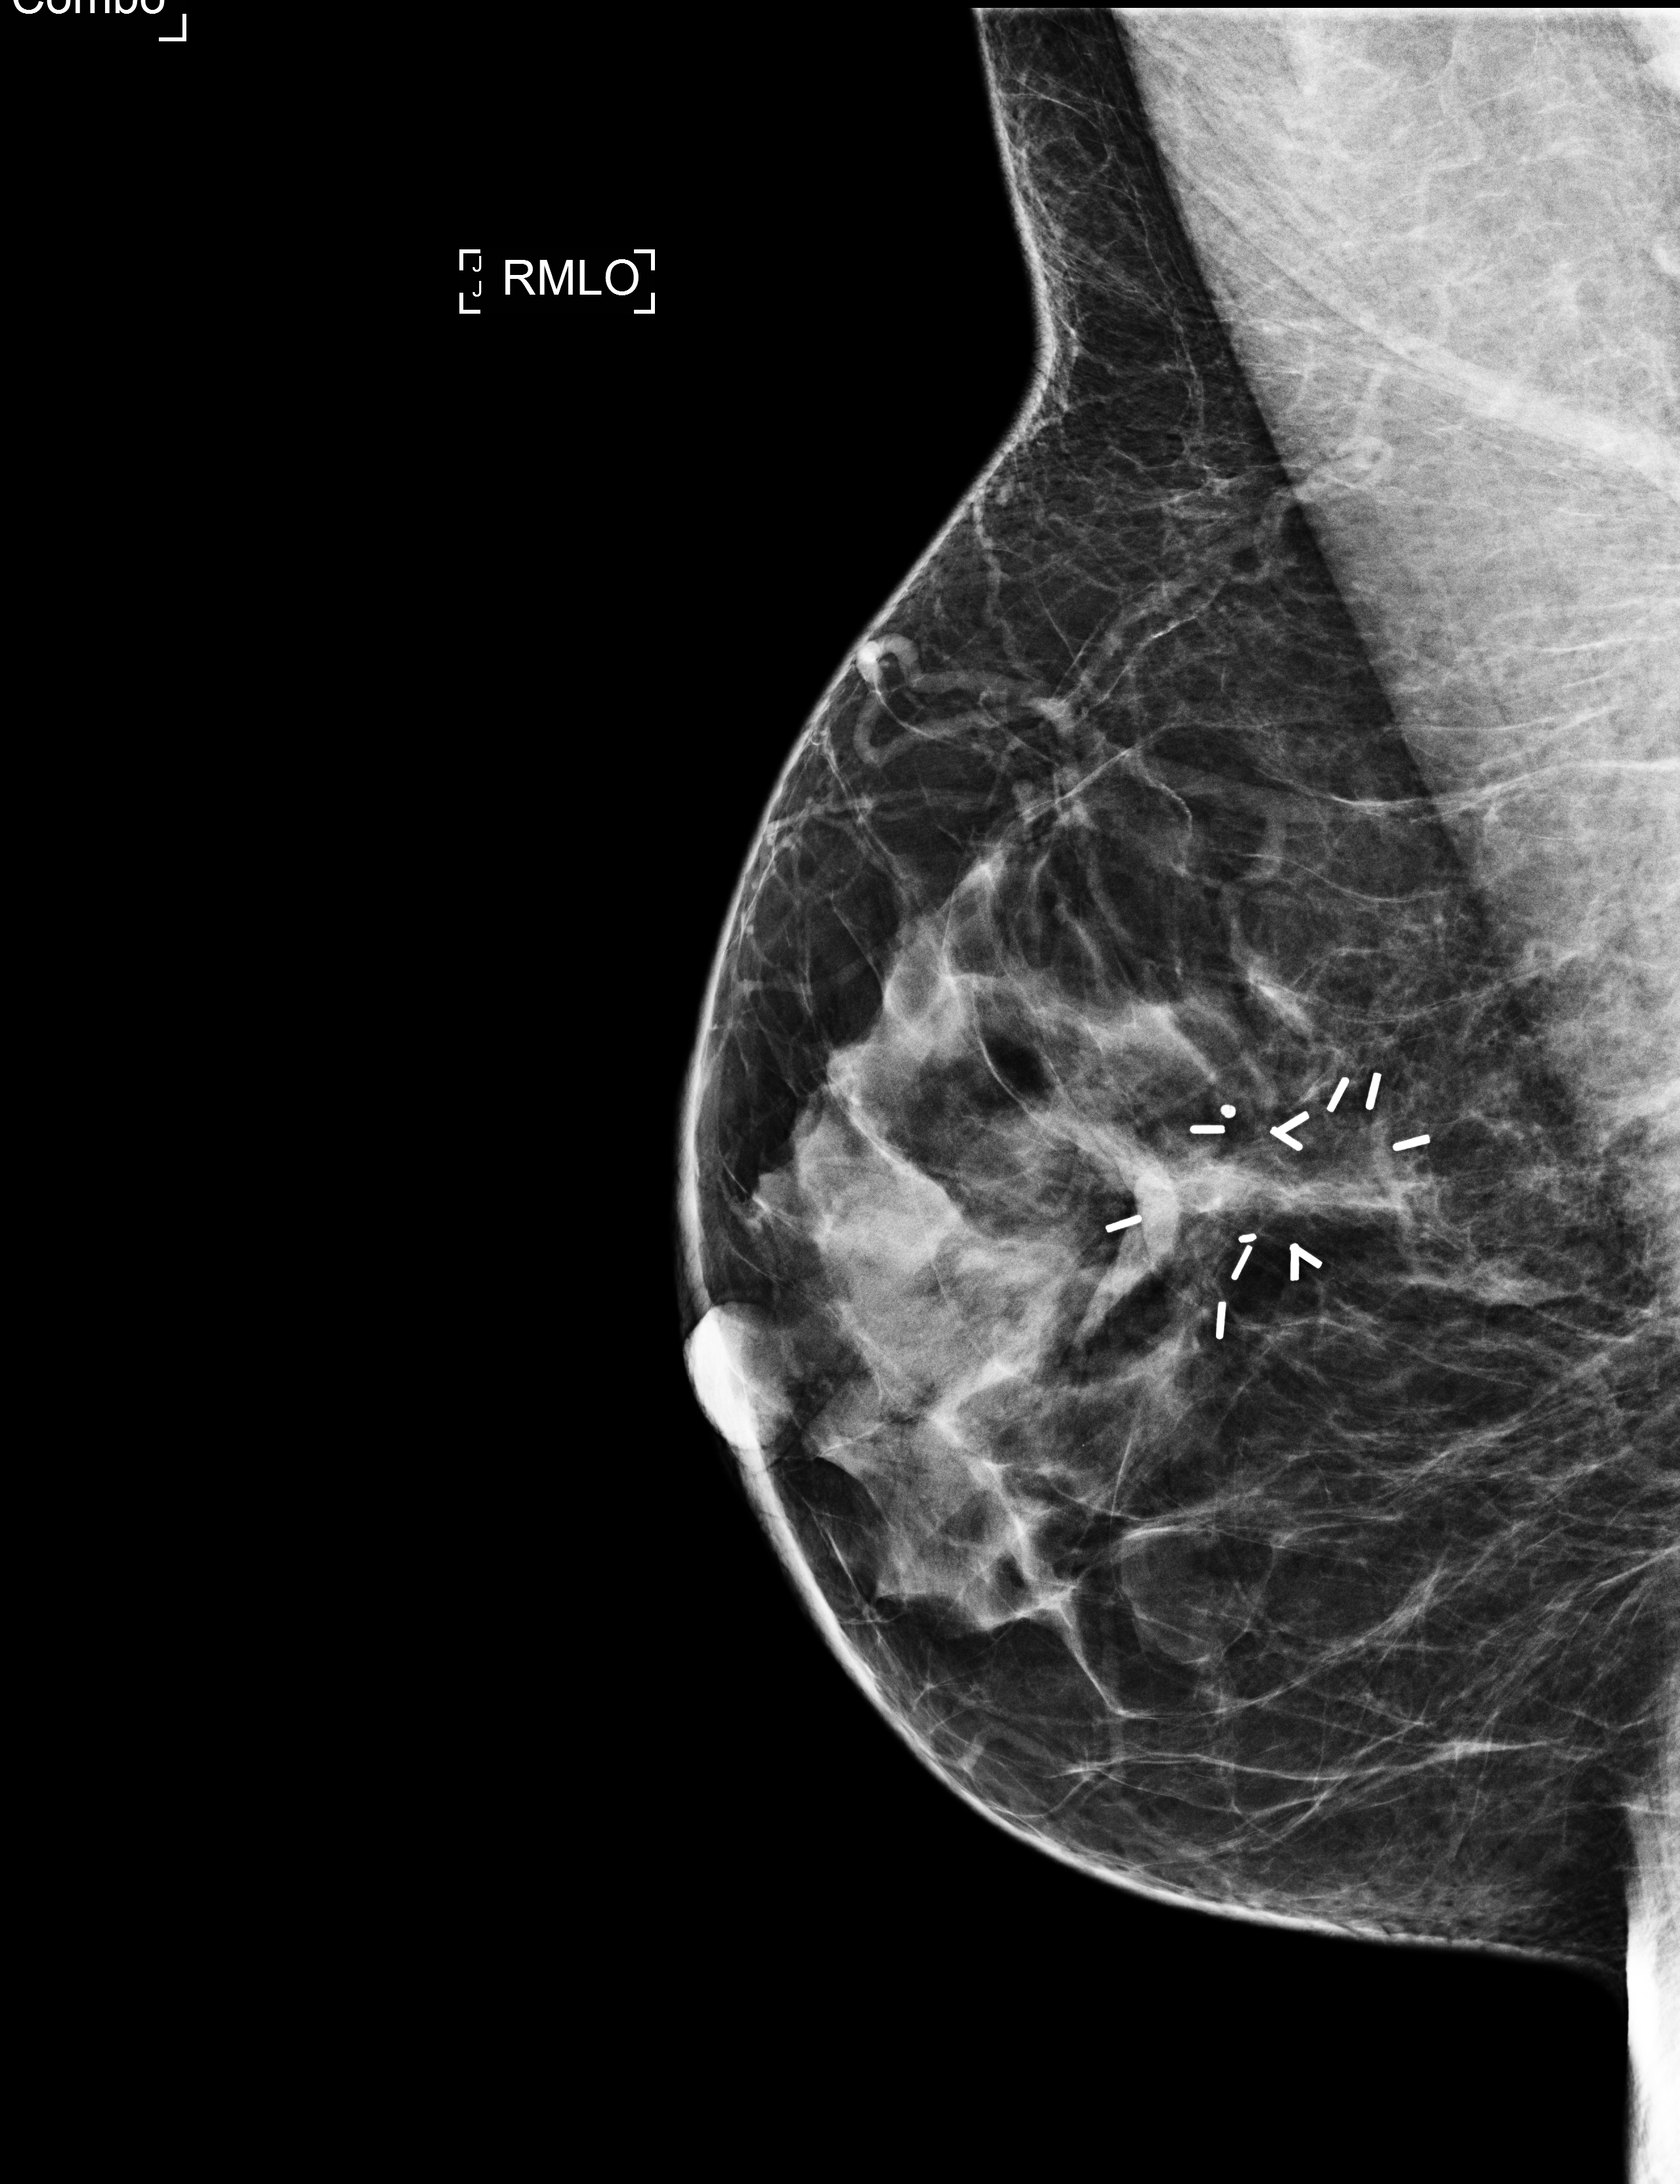
Full-field digital mammogram (FFDM), right breast, mediolateral oblique (MLO) view, screening examination, system: Selenia Dimensions. Patient aged 48 years (female).
Breast density at the screening exam (both breasts): heterogeneously dense (BI-RADS density category c). Final BI-RADS category for the screening round (tomosynthesis exam, both breasts): category 1. Recall: no recall after this screen.